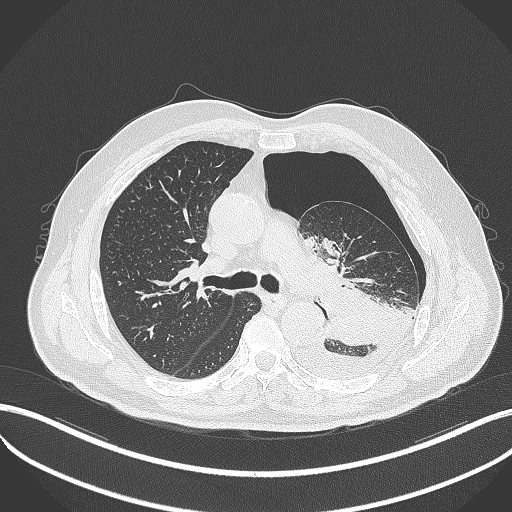
Chest CT, one axial slice; slice 329 of 464 in the series (ordered by position); reconstruction kernel B70f; lung window (W 1500 / L -600 HU); 1 mm slice thickness; 512 × 512 image matrix, field of view 400 × 400 mm. Patient: male, 76 years. From the clinical record (not read from this slice): clinical TNM (as recorded): T3 N0 M1b.
Structures marked on this image (rectangle marked by the reading radiologist):
- lung tumour (recorded histology: adenocarcinoma): bounding box <319,293,396,349> (left, top, right, bottom; pixels)